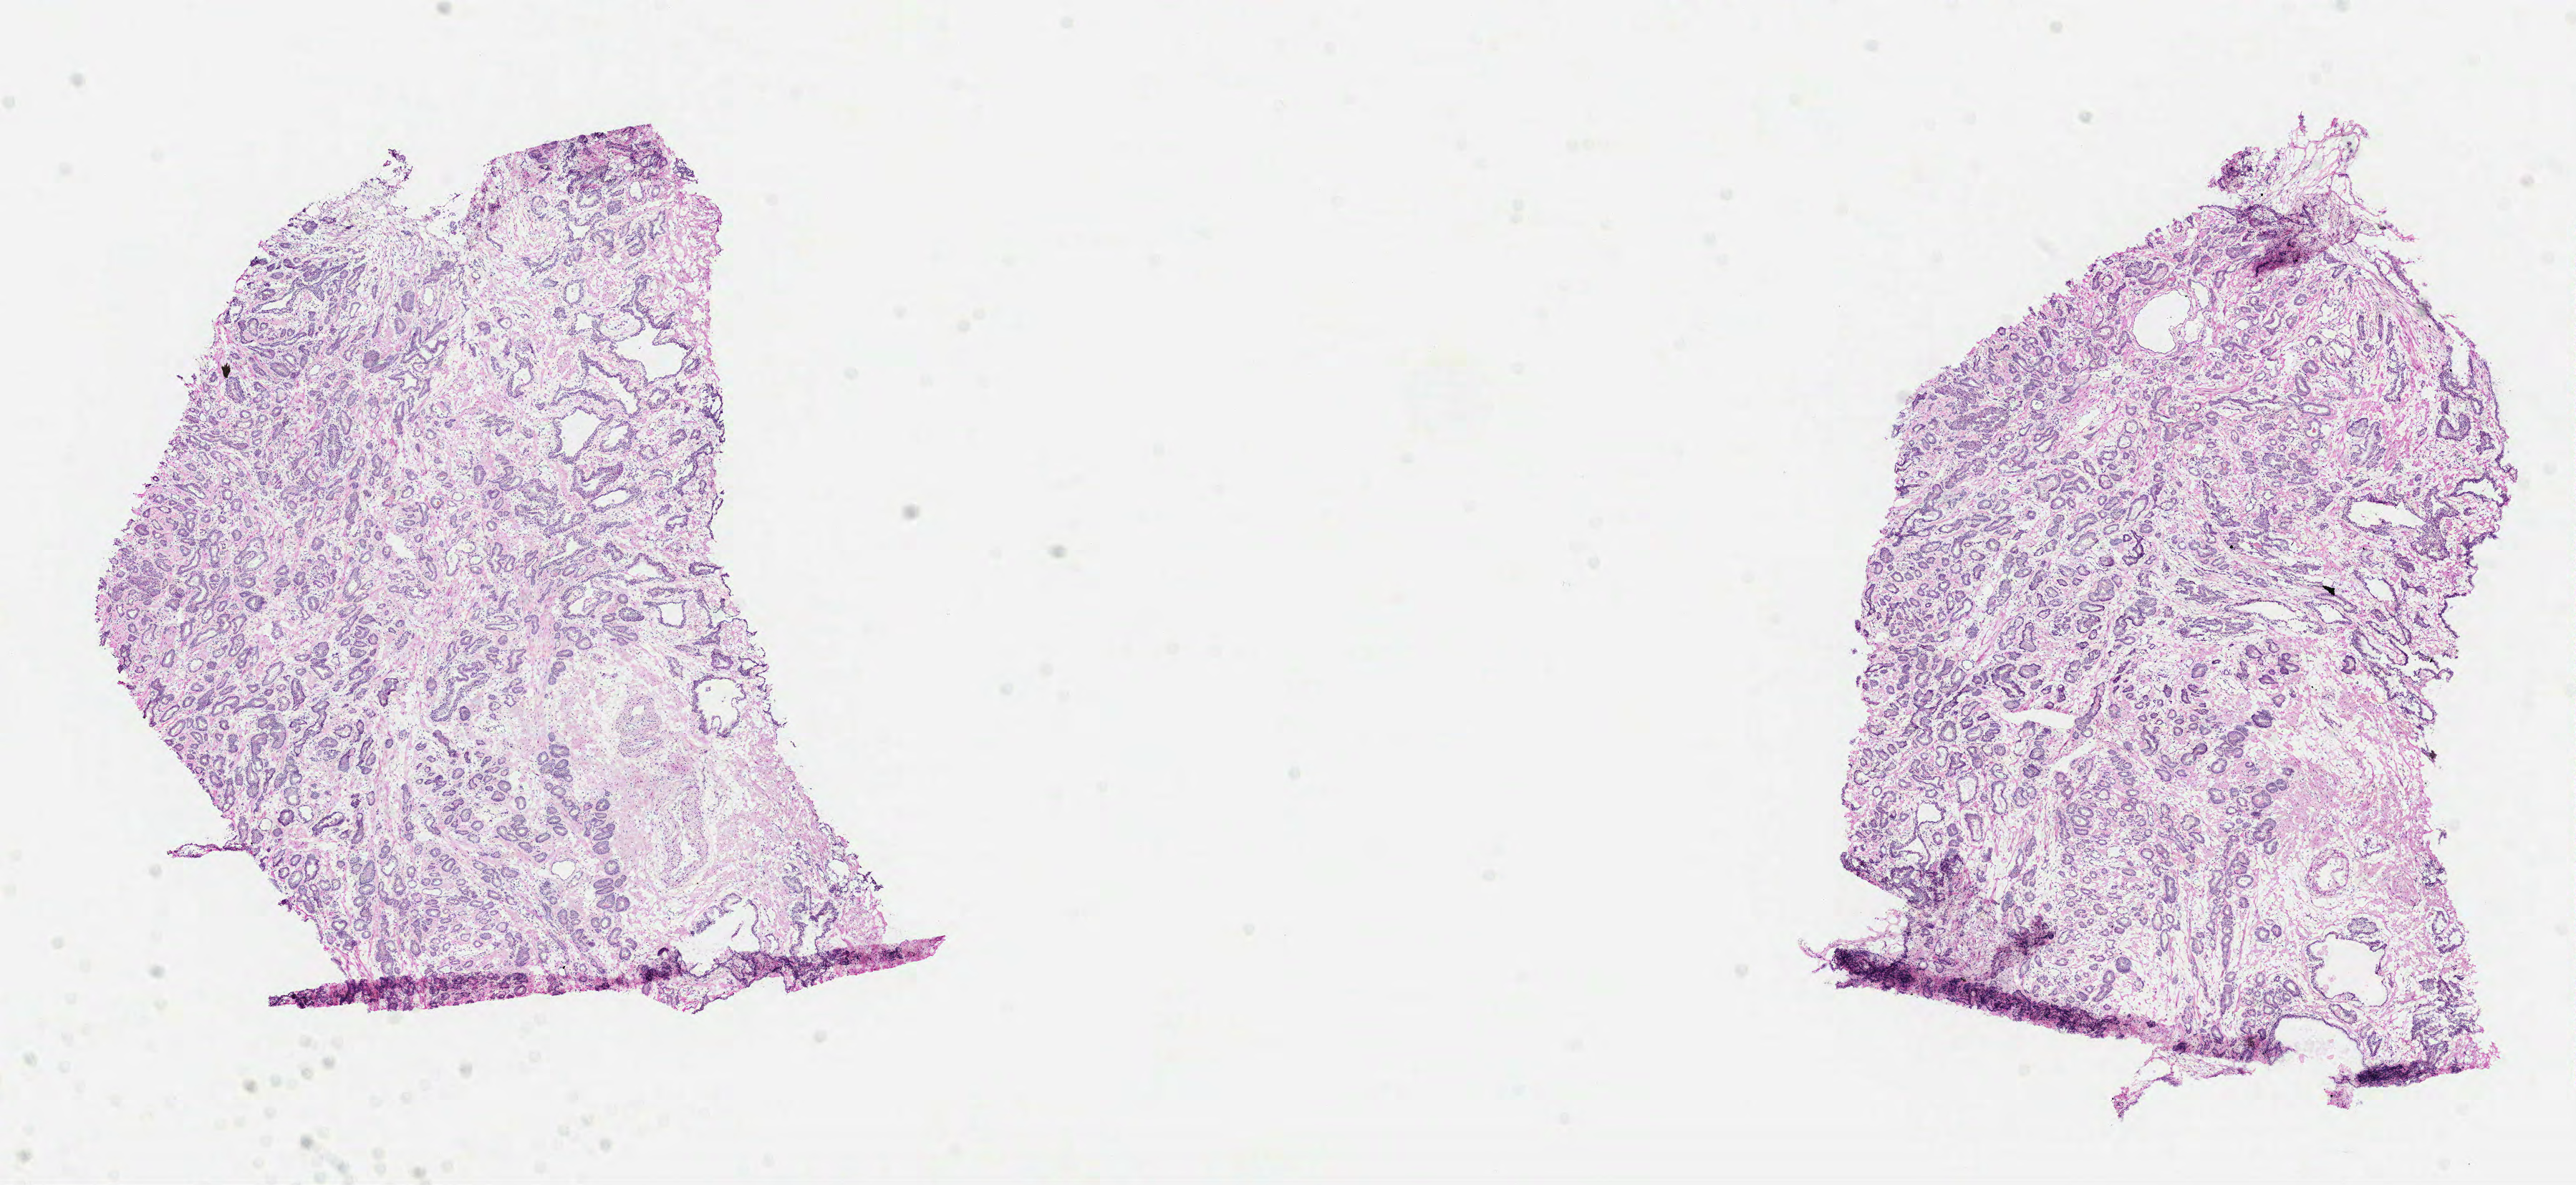
Whole-slide histology image, Hematoxylin and eosin (H&E) stained, a low-resolution overview of the entire scanned area, about 14.5 x 6.7 mm (from a 40x scan), FFPE section, primary tumour sample from the prostate. Male, age 57 years at initial diagnosis. Gleason score: 7 (3+4).
• laterality: bilateral
• pathologic diagnosis: Acinar cell carcinoma (prostate gland)